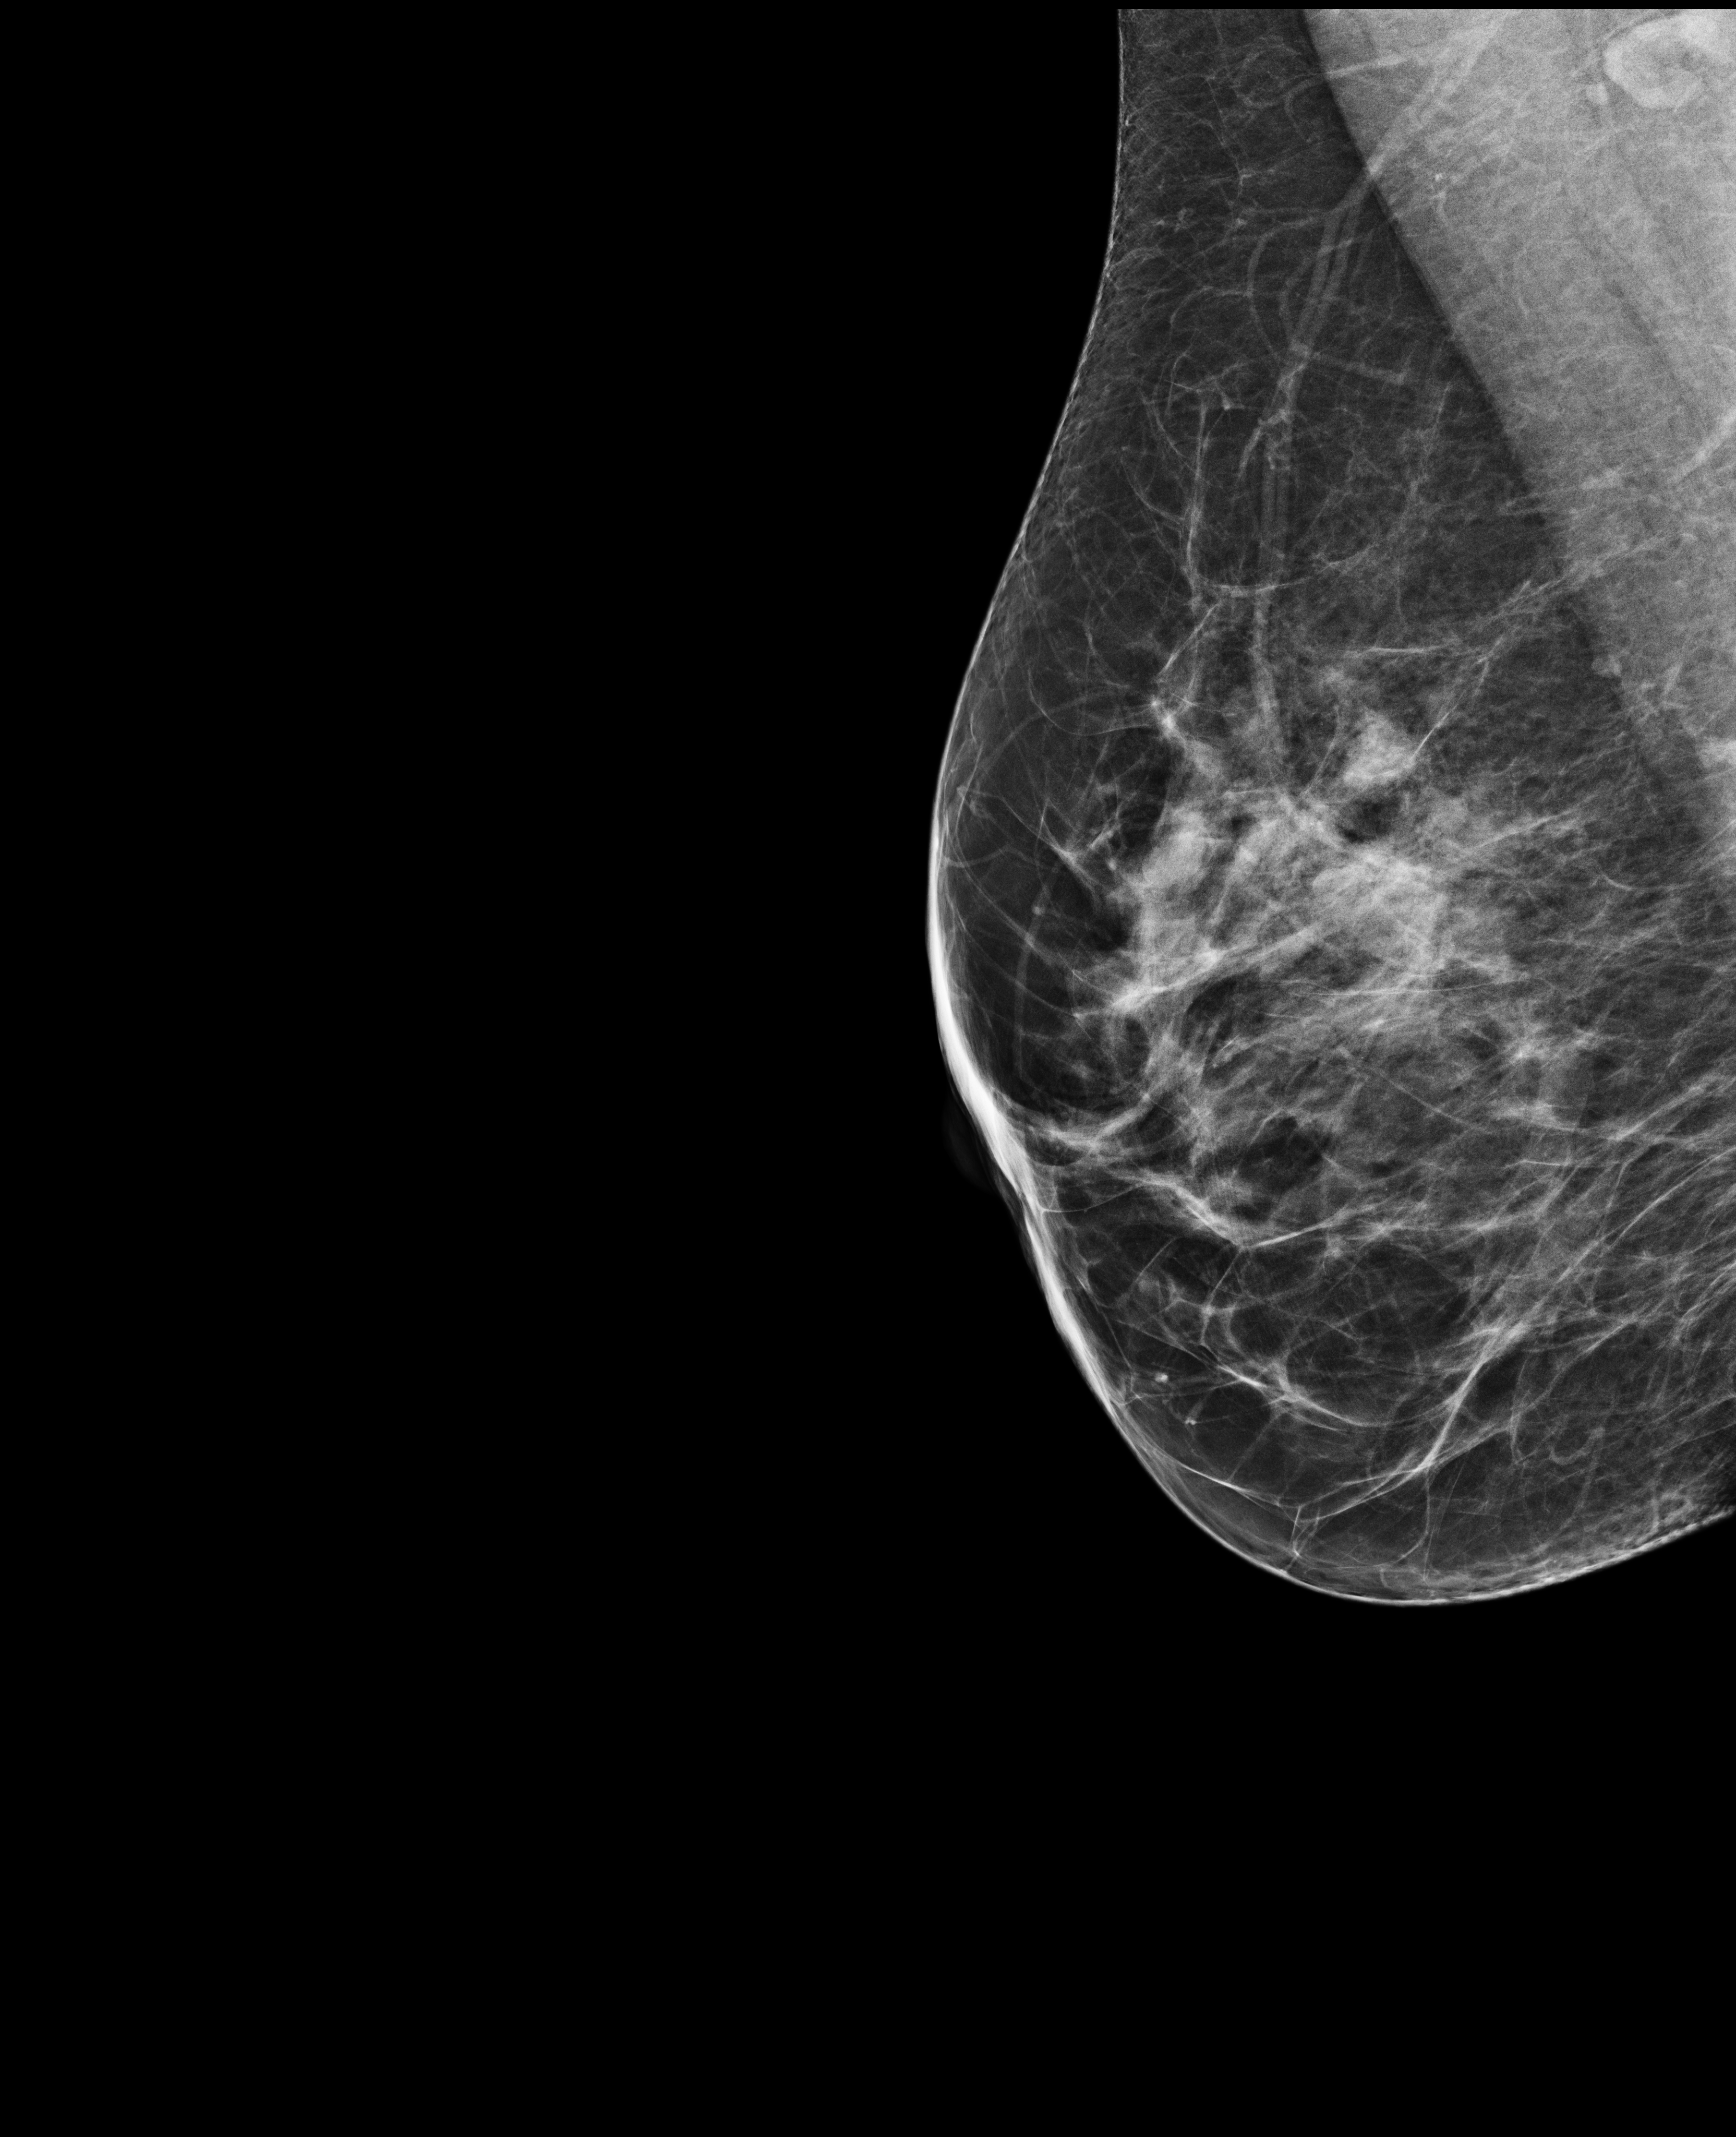
Full-field digital mammogram (FFDM); right breast; mediolateral oblique (MLO) view; annual screening mammography examination; system: Selenia Dimensions. Female patient, age 44 years.
BI-RADS breast density category at the screening exam (both breasts, scale 1–4): 3. Final BI-RADS category for the screening round (tomosynthesis exam, both breasts): category 2. Recall: recalled for additional imaging after this screen.